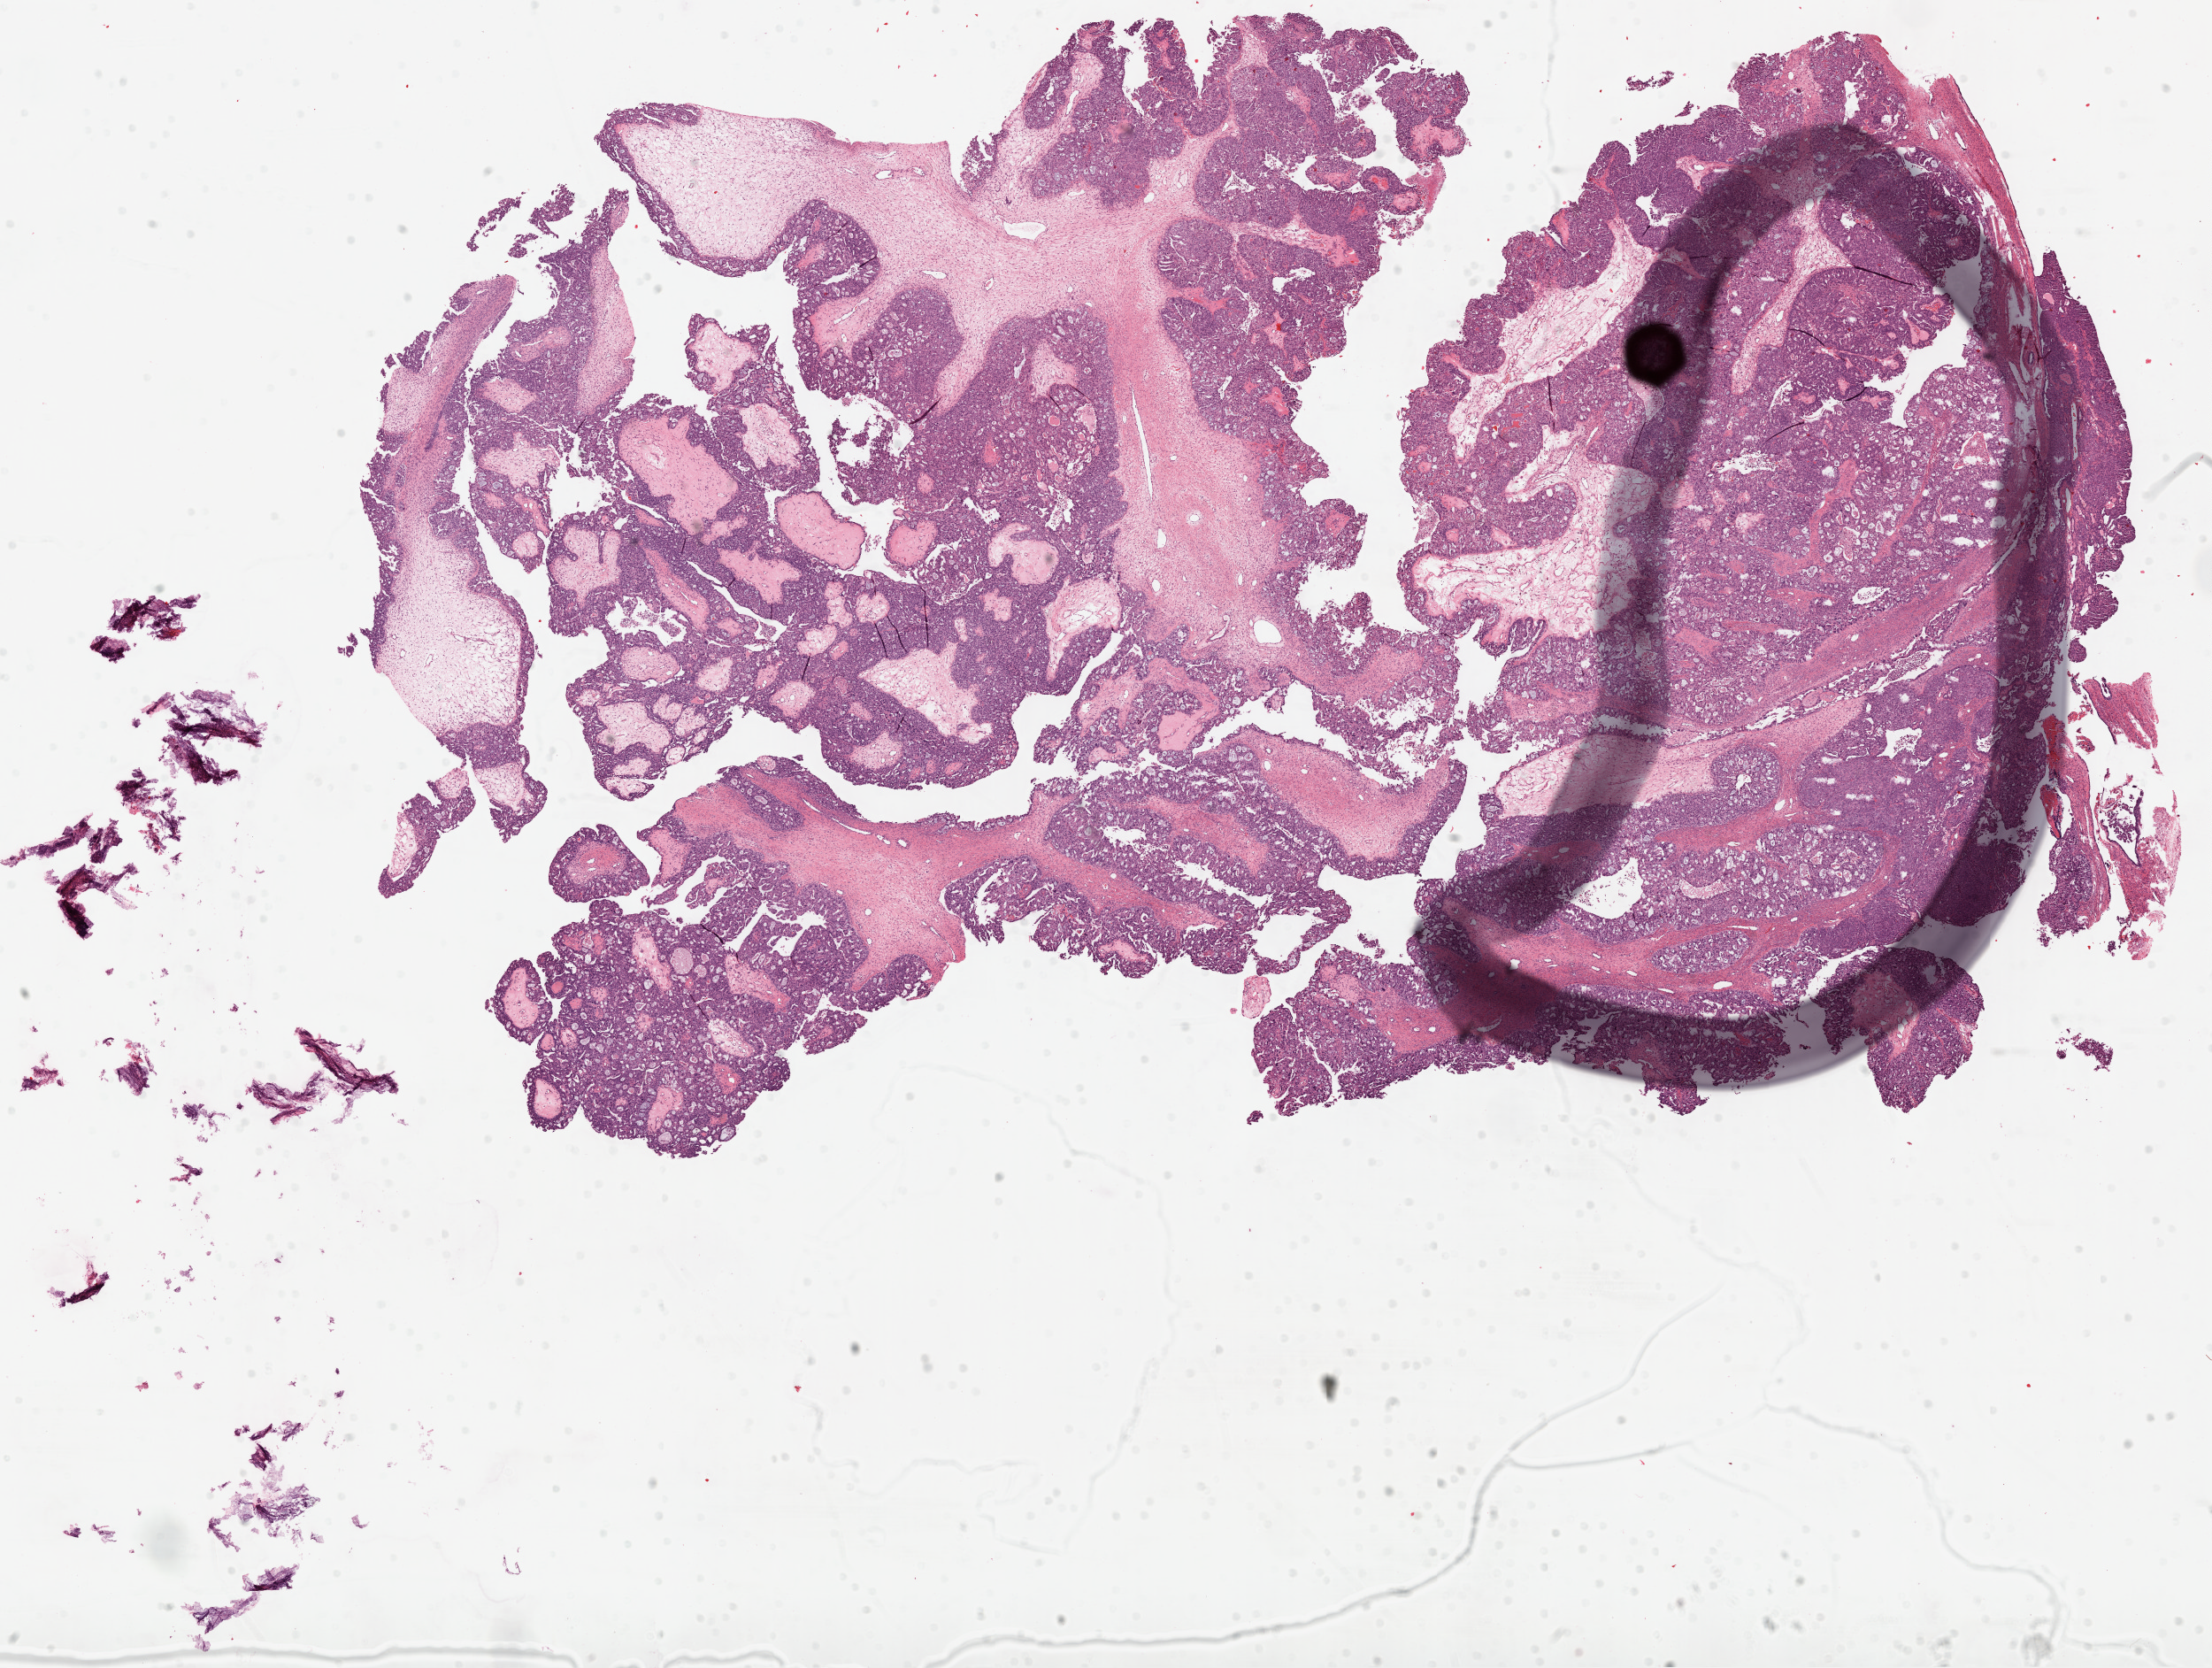
H&E whole-slide image, shown as a low-resolution overview of the whole scanned area (about 20.1 x 15.1 mm, acquisition: 20x scan), frozen section from the top of the tissue portion, ovary, primary tumour sample. Patient: female, age at initial diagnosis 55 years. Histologic grade: G3 (poorly differentiated). Composition of this section per pathologist review: tumour cells 70%, tumour nuclei 80%, normal cells 0%, stromal cells 20%, necrosis 10%.
* laterality: right
* diagnosis: Serous cystadenocarcinoma, NOS
* FIGO stage: IIIC